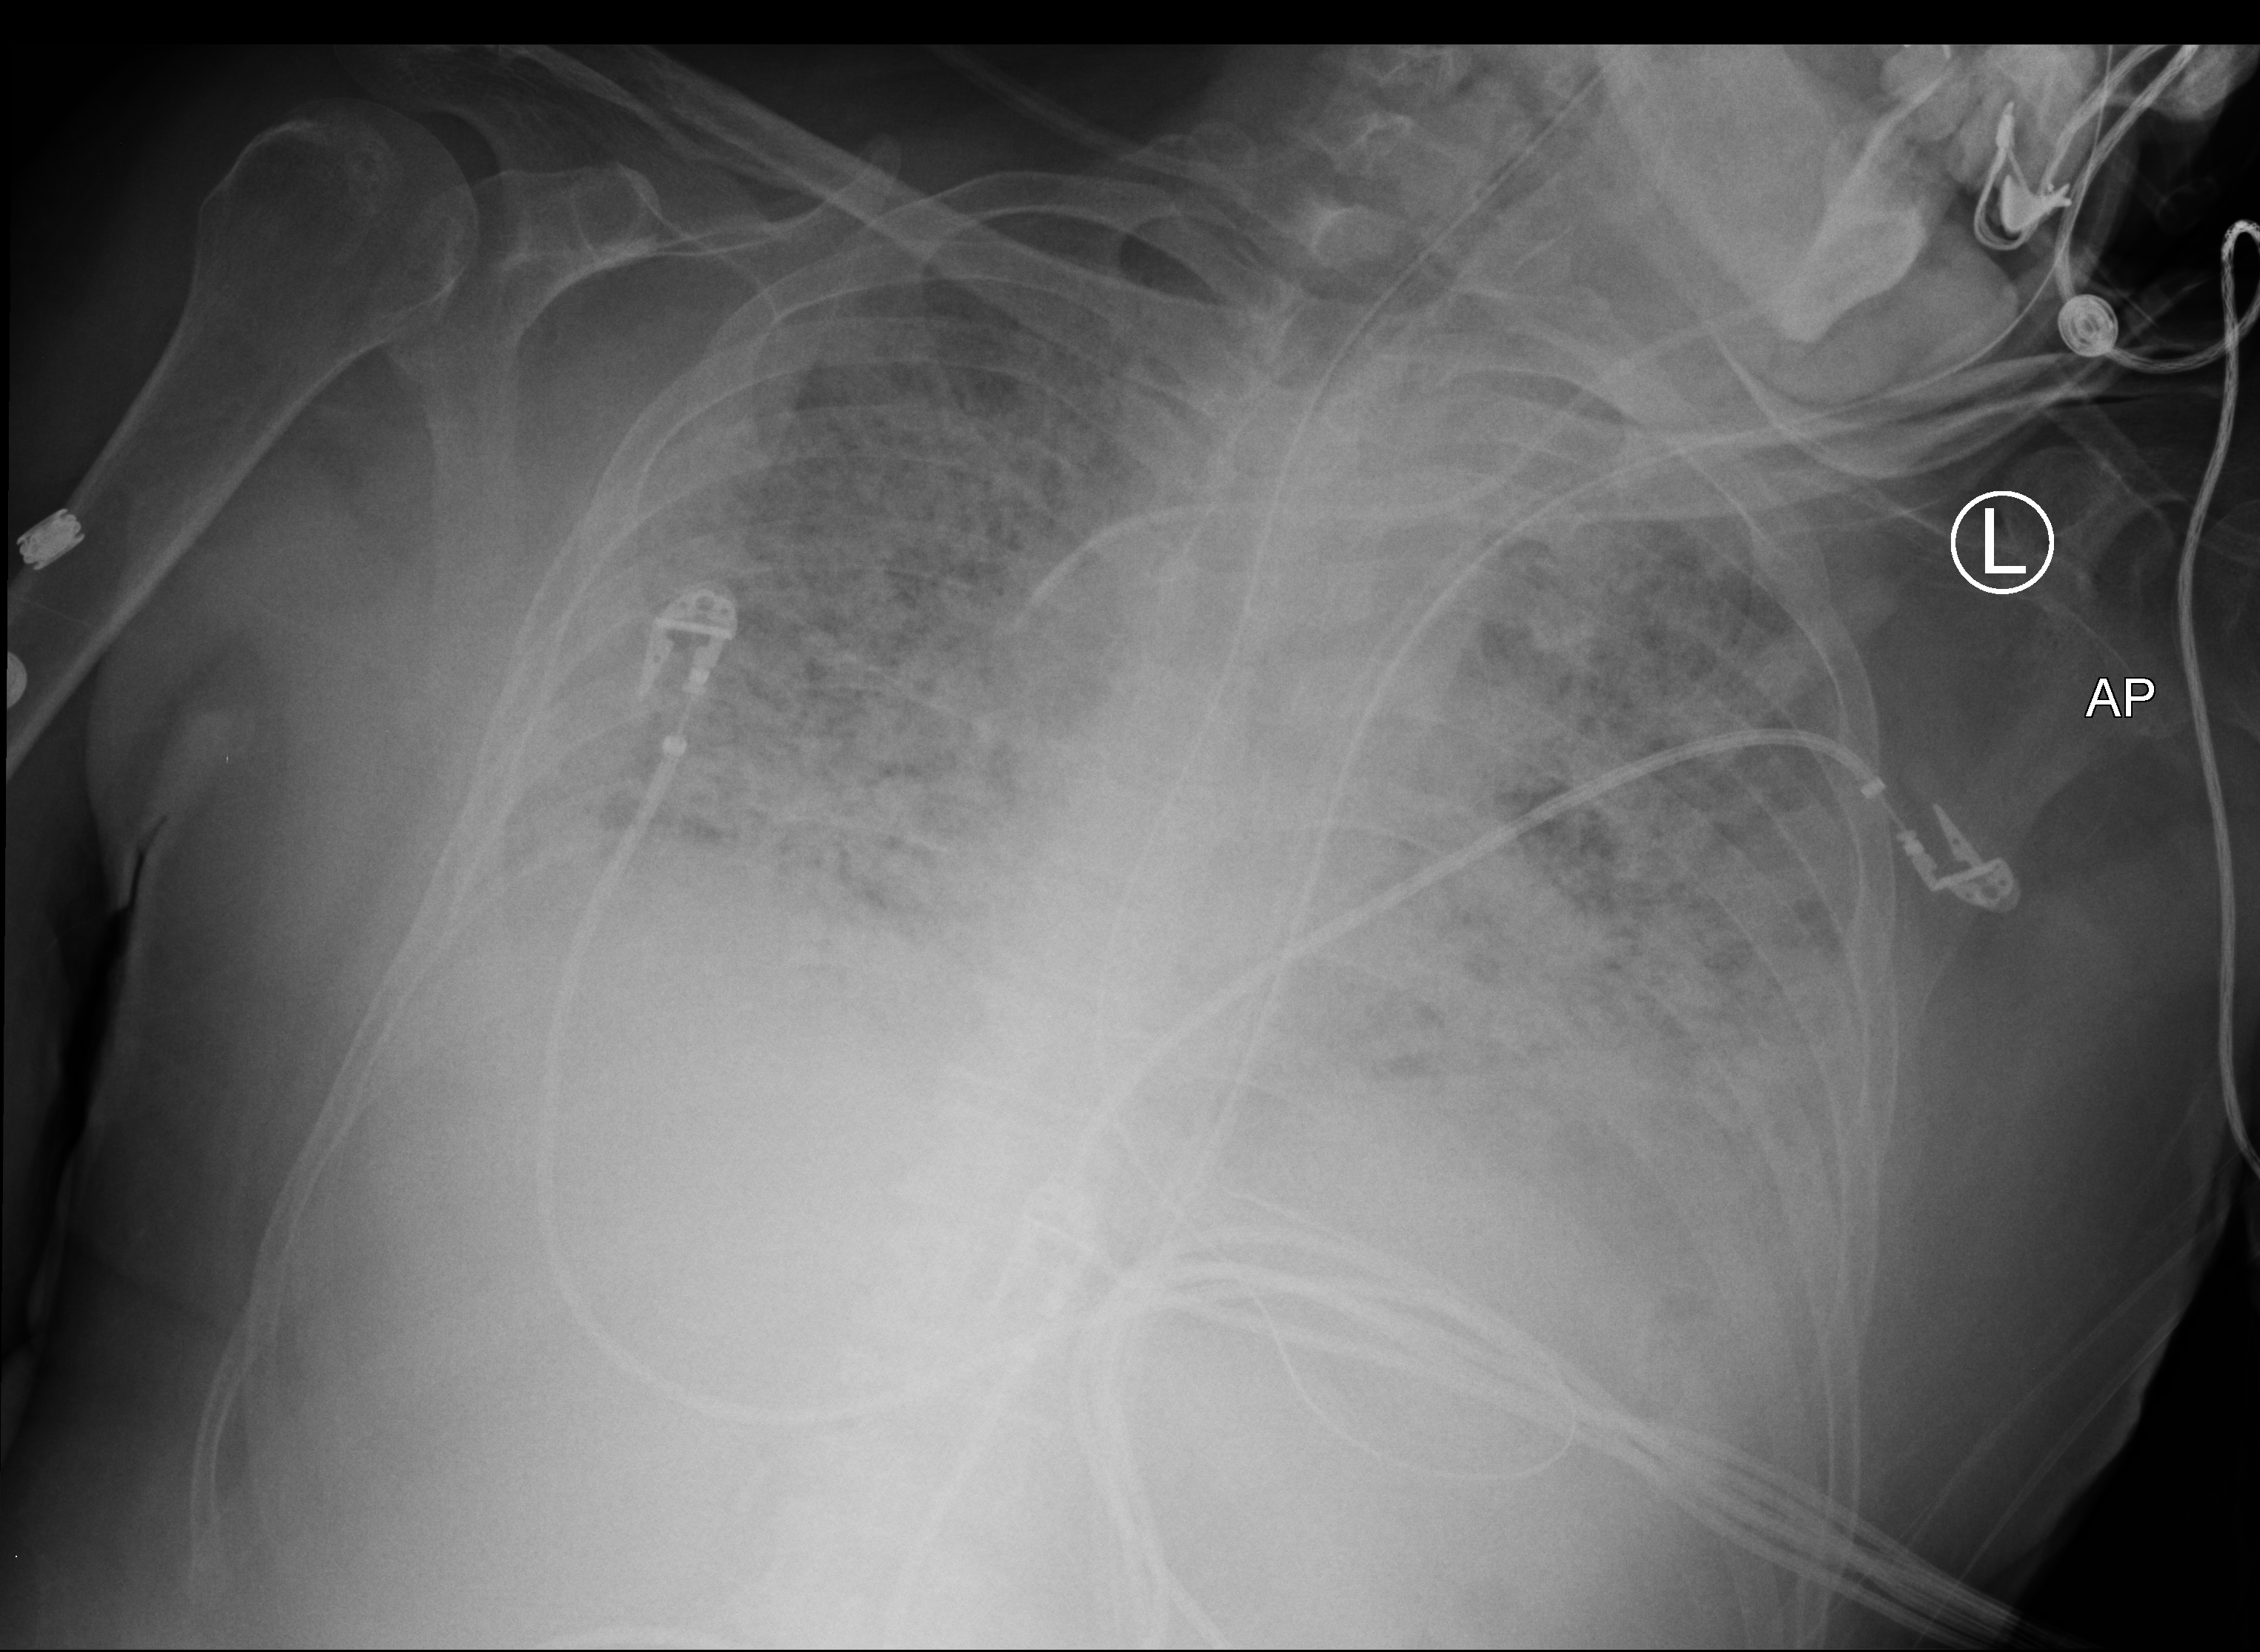
Portable chest radiograph, anteroposterior (AP) projection. Patient hospitalised with COVID-19; male, aged 60–74 years.
From the hospital-stay record, not from the radiograph (when in the stay this image was taken is not recorded): diabetes (admission record): no.